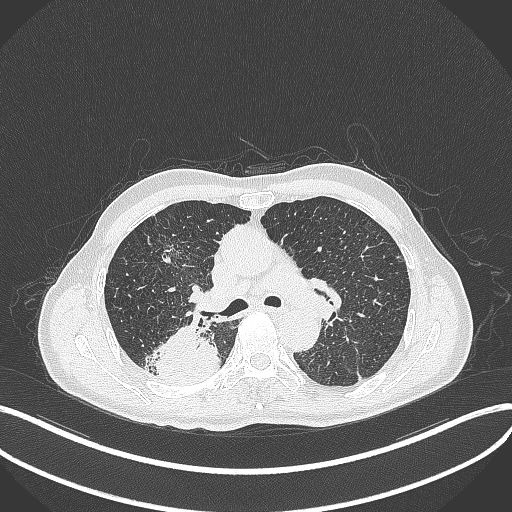
Chest CT, one axial slice. Position 290 of 428 along the scan axis. Reconstruction kernel B70f. 120 kVp. Lung window (W 1500 / L -600 HU). 1 mm slice thickness. 512 × 512 image matrix, field of view 400 × 400 mm. Male patient, age 79 years. From the clinical record (not read from this slice): clinical TNM (as recorded): T3 N0 M0.
Structures marked on this image (rectangle marked by the reading radiologist):
- lung tumour (recorded histology: adenocarcinoma): bounding box <153,324,222,383> (left, top, right, bottom; pixels)